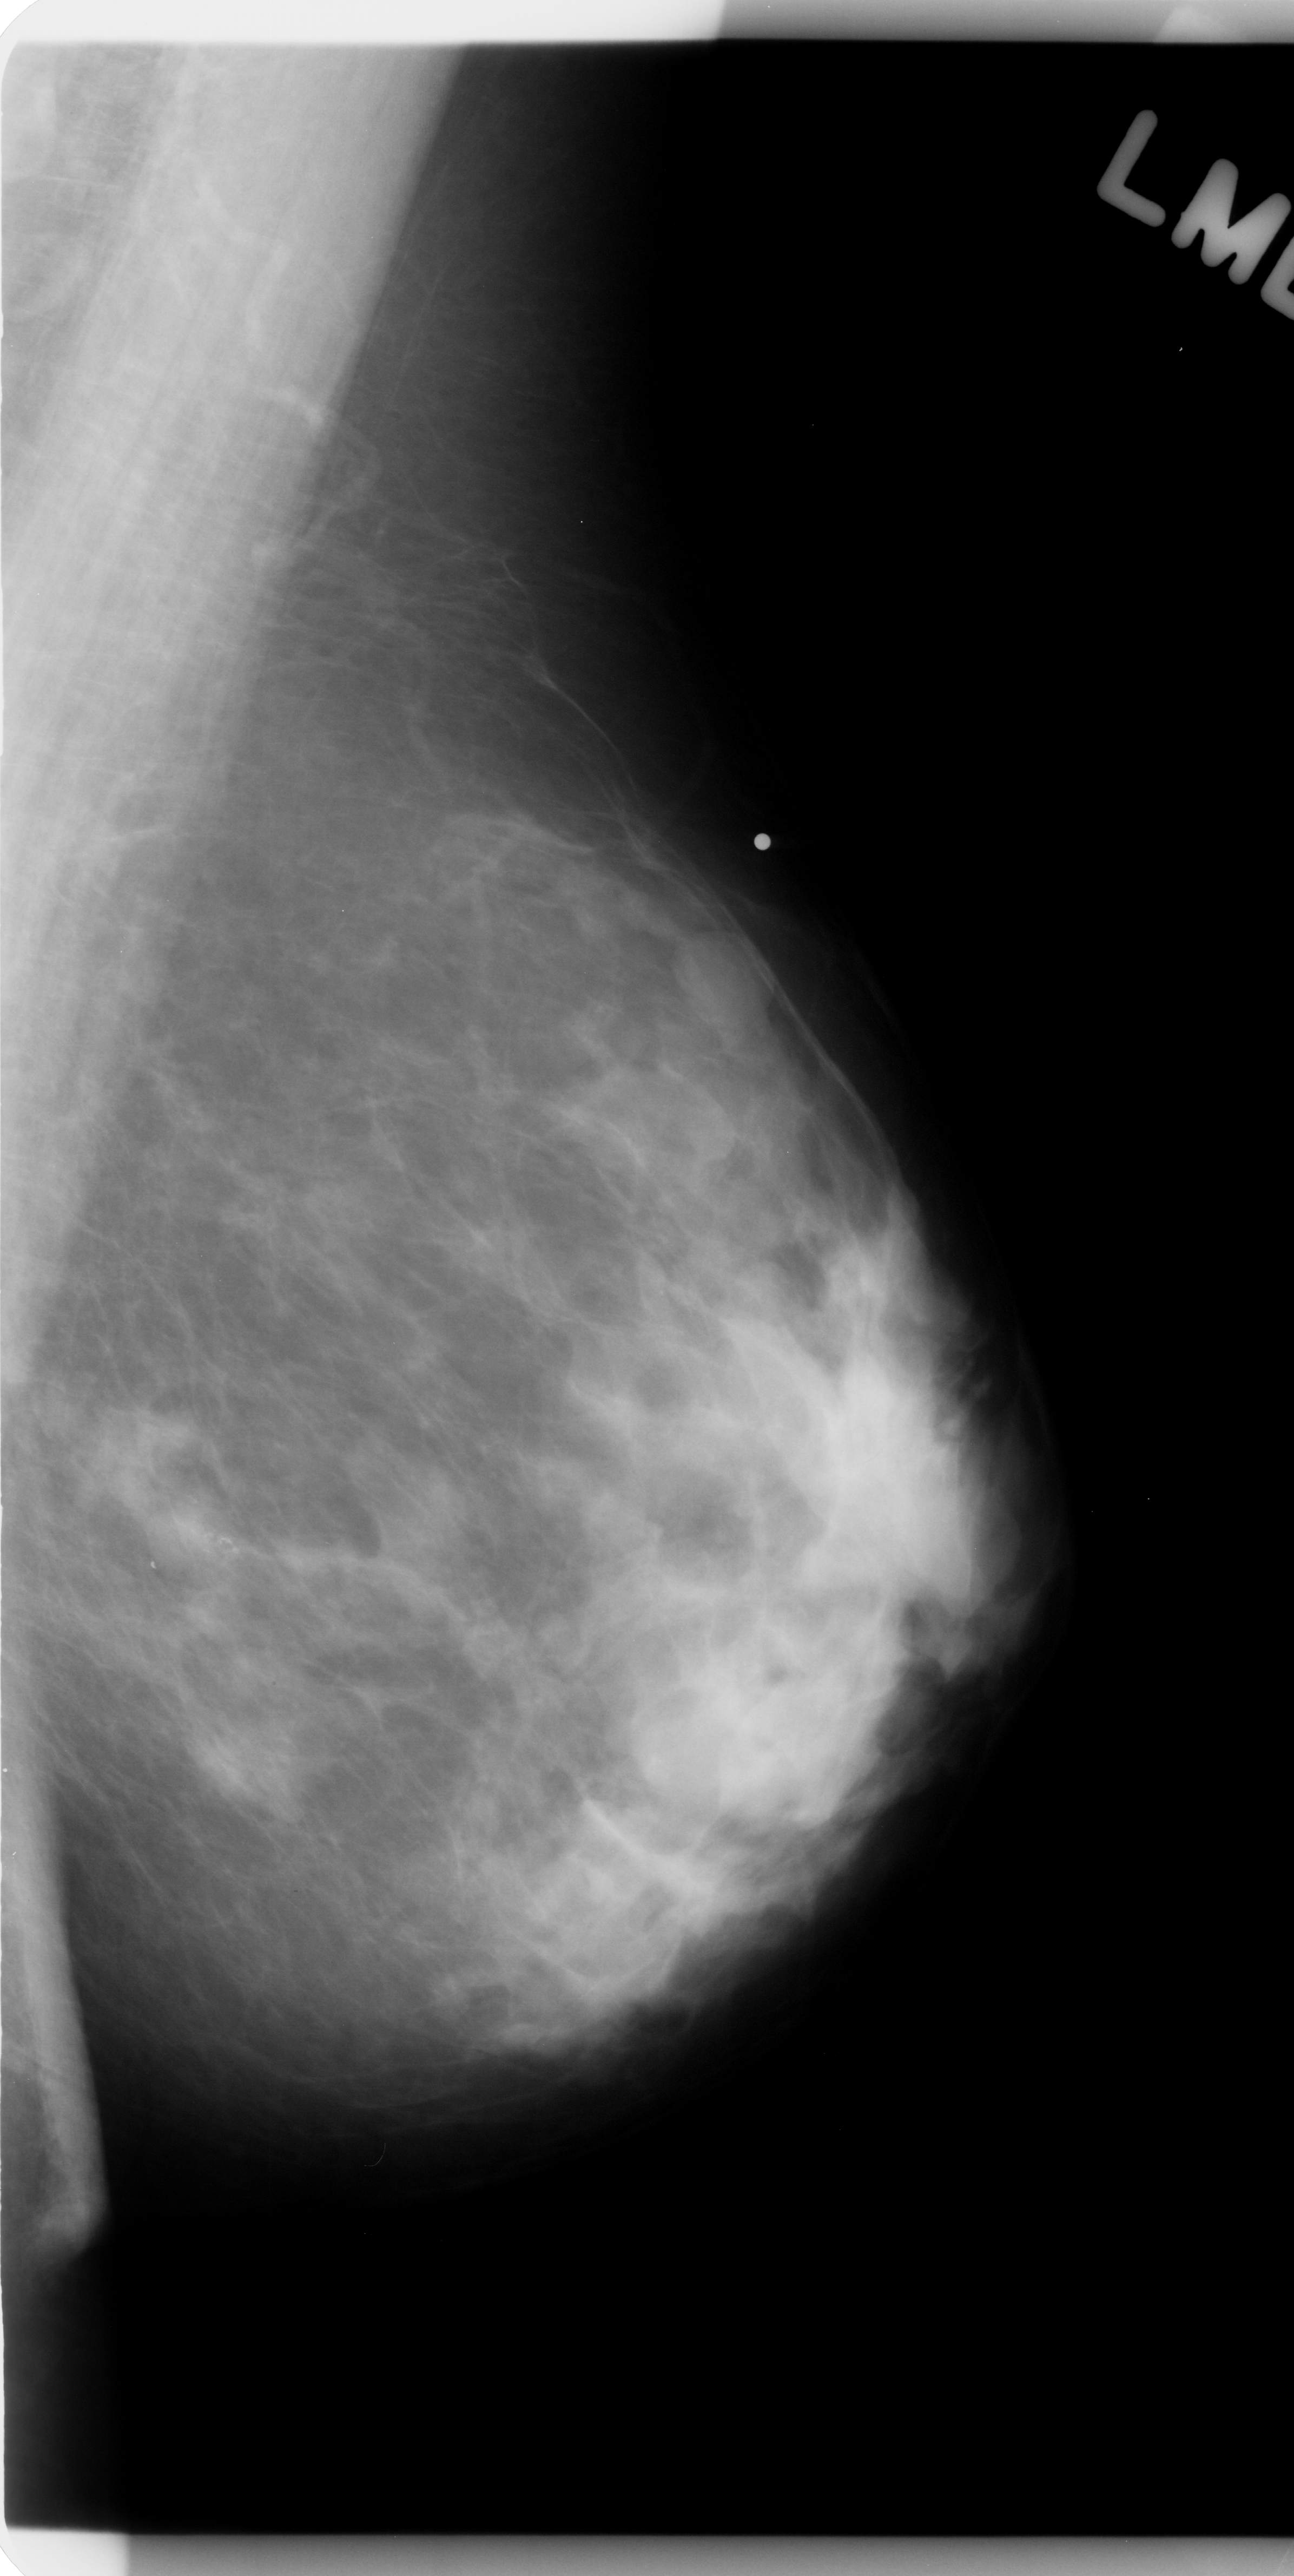
Scanned film-screen mammogram; left breast; mediolateral oblique (MLO) view; breast composition: heterogeneously dense (BI-RADS density category 3 of 4); 1294 × 2576 image matrix.
Expert-marked regions of interest on this film, with their recorded descriptors:
- mass, shape oval, margins circumscribed; BI-RADS assessment category 3; subtlety rating 5 on a 1 (subtle) to 5 (obvious) scale; pathology result (as recorded, not read from the image): benign: bounding box <670,929,780,1057> (left, top, right, bottom; pixels)